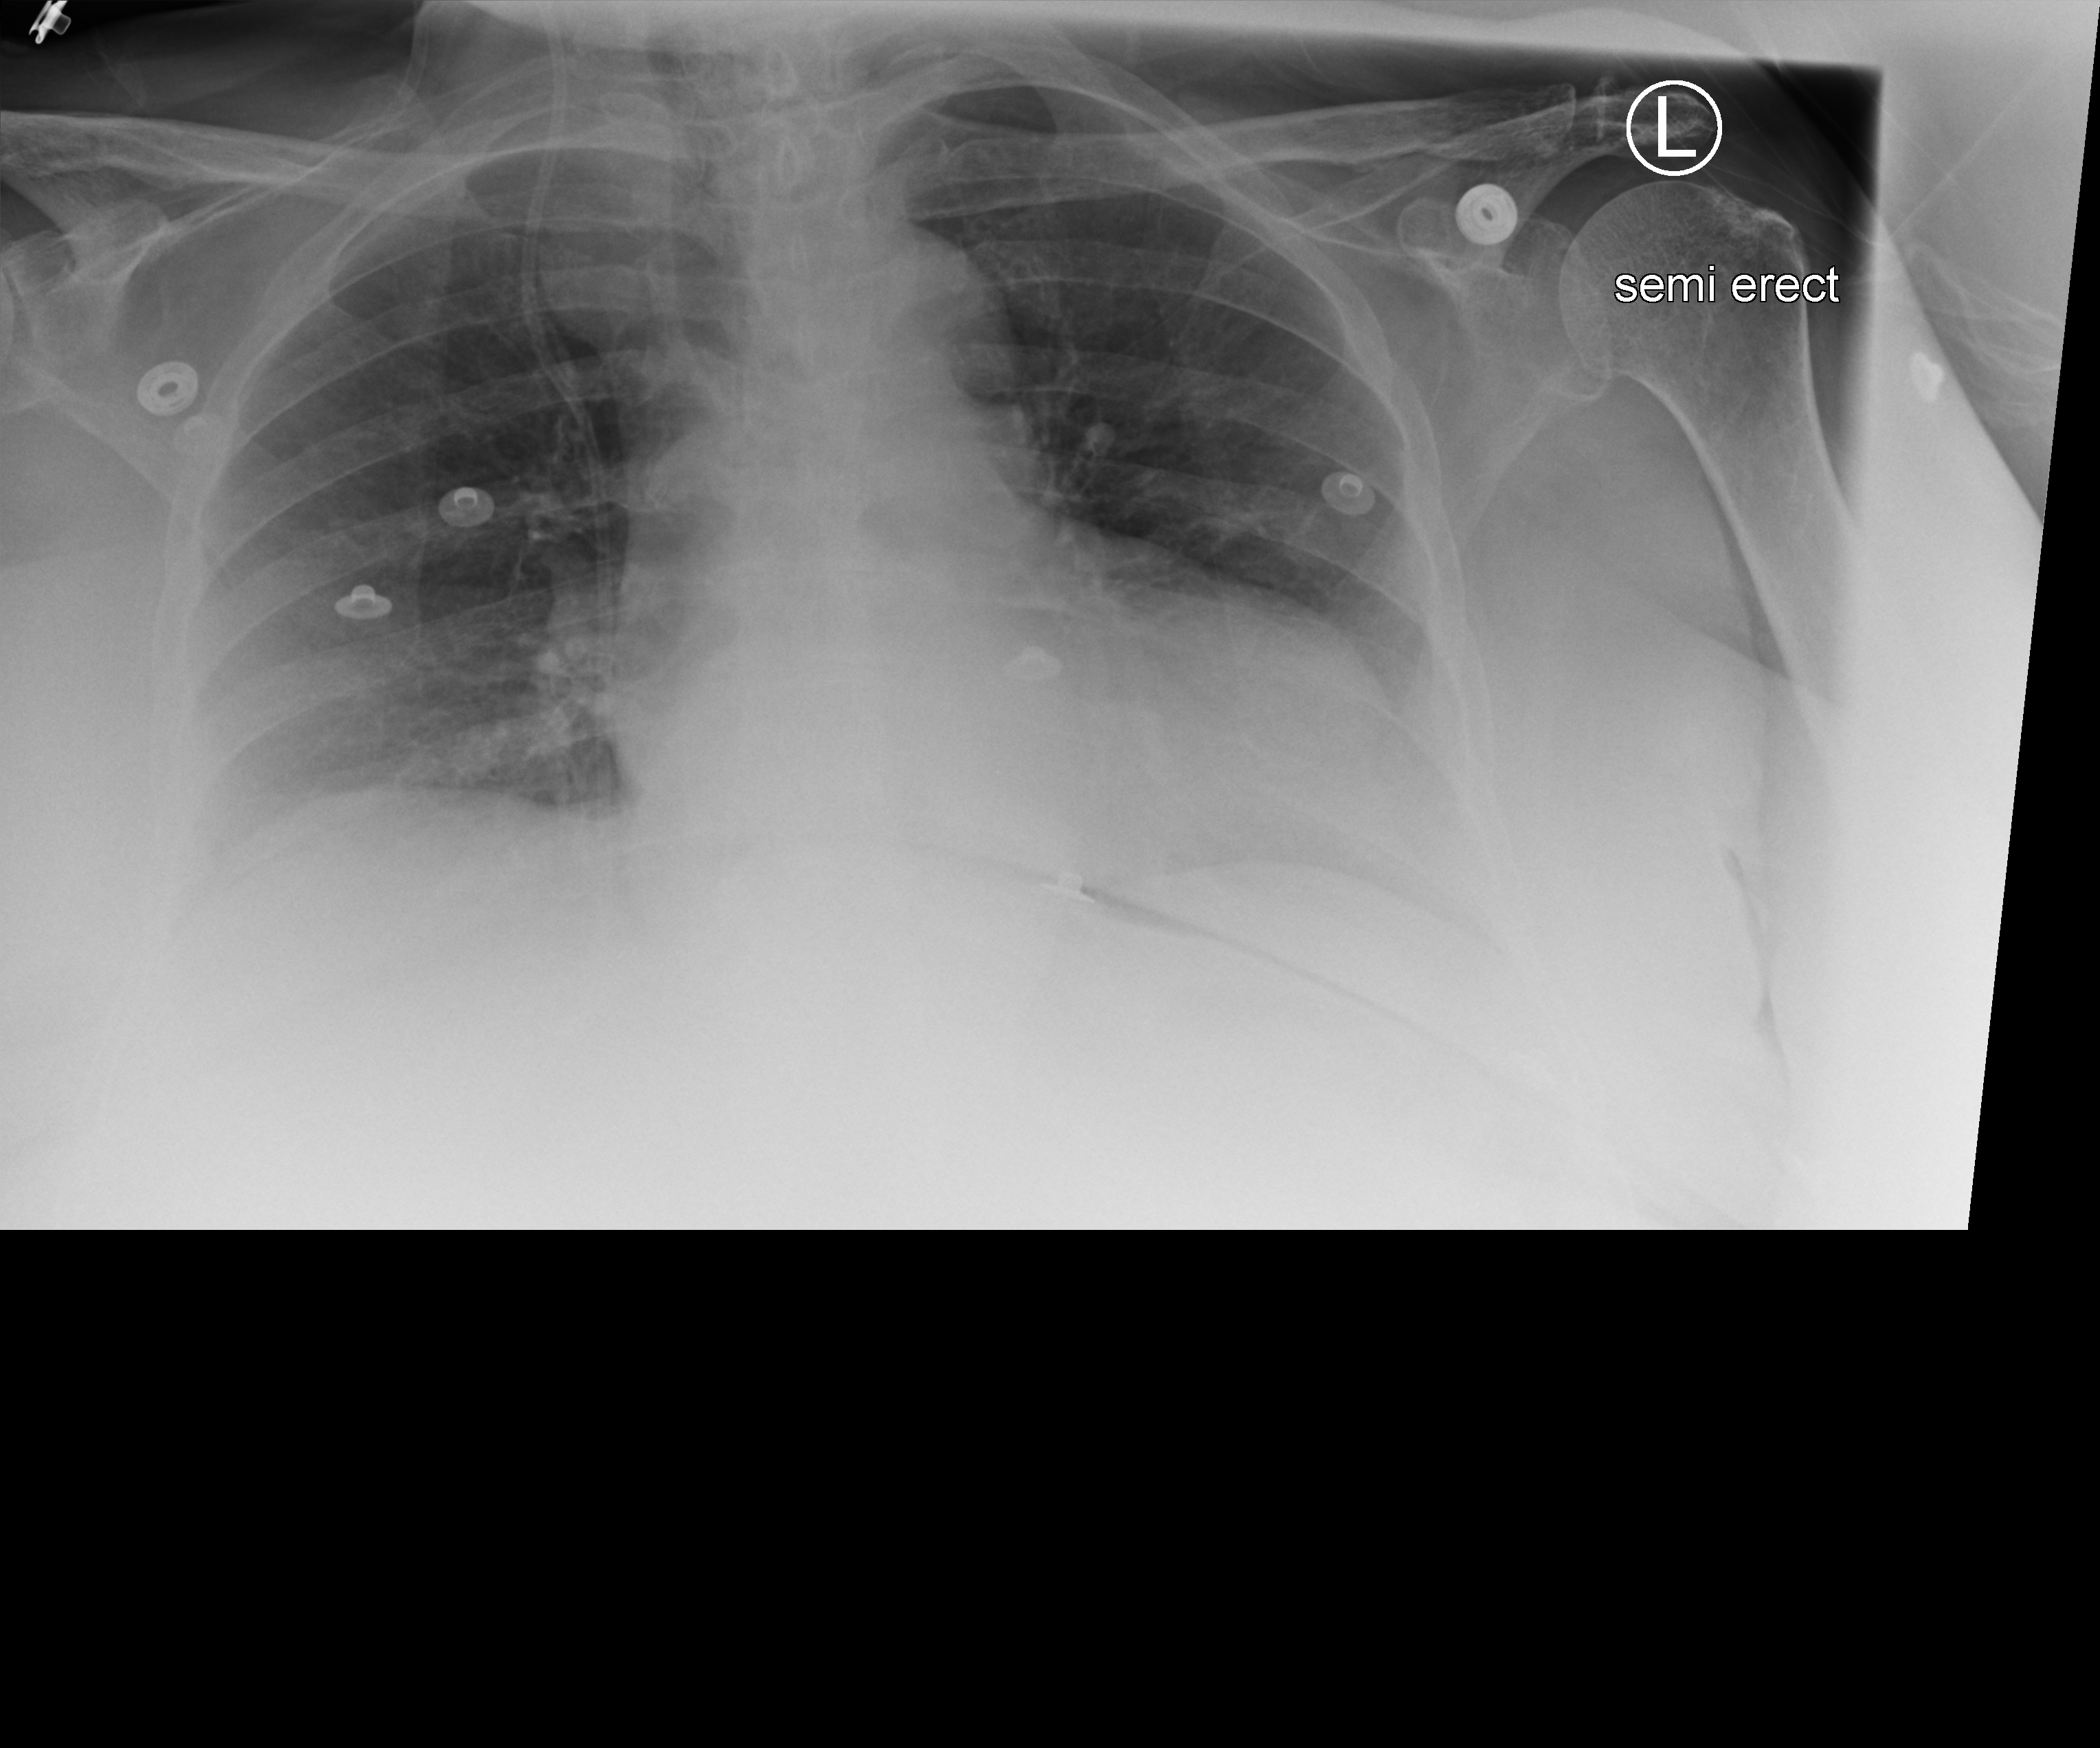
Chest X-ray; anteroposterior (AP) projection. Female patient hospitalised with COVID-19, age 75–90 years.
From the hospital-stay record, not from the radiograph (when in the stay this image was taken is not recorded): hypertension (admission record): yes.